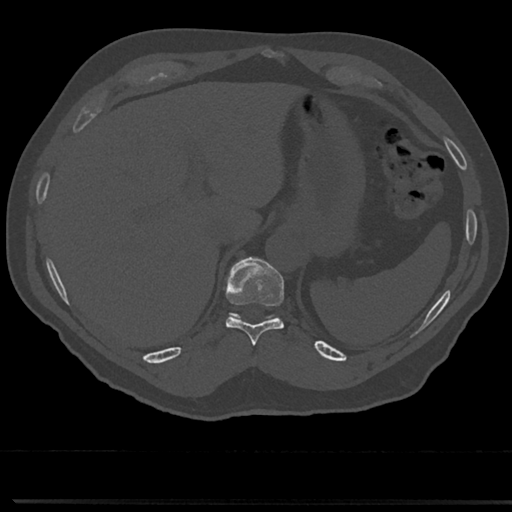
CT including the spine, one axial slice. Position 247 of 817 along the scan axis. Reconstruction kernel Br40s/3. Bone window (W 1800 / L 400 HU). 0.5 mm slice thickness. 512 × 512 image matrix. Male patient, age 61 years. From the clinical record (not read from this slice): primary cancer: prostate.
Structures marked on this image (semi-automatically segmented with operator editing):
- T10 vertebra: bounding box <223,257,287,343> (left, top, right, bottom; pixels)
- T9 vertebra: <250,353,259,366>